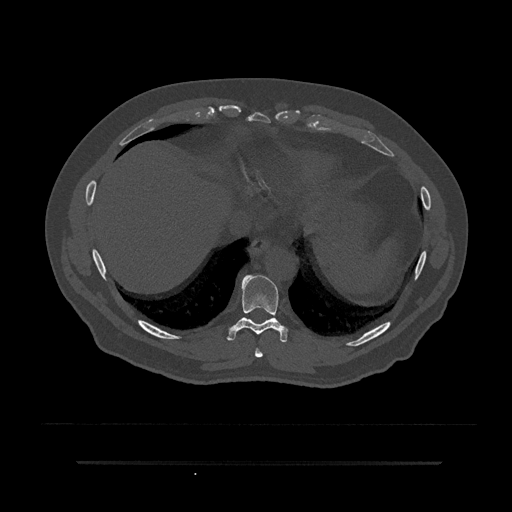
CT including the spine, one axial slice; slice 376 of 797 in the series (ordered by position); 120 kVp; bone window (W 1800 / L 400 HU); 512 × 512 image matrix, field of view 464 × 464 mm. Male patient, age 59 years. From the clinical record (not read from this slice): primary cancer: bile ducts.
Annotated regions visible in this slice (semi-automatic segmentation, software-assisted and operator-edited):
- T8 vertebra: bounding box <255,348,263,358> (left, top, right, bottom; pixels)
- T9 vertebra: <227,275,289,343>